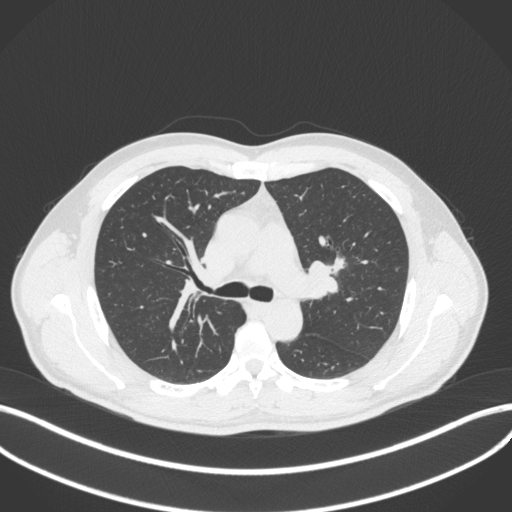
Chest CT, one axial slice. Position 274 of 383 along the scan axis. Reconstruction kernel B31f. Lung window (W 1500 / L -600 HU). 1 mm slice thickness. 512 × 512 image matrix, field of view 400 × 400 mm. Male patient, age 50 years. Case-level facts recorded for this patient, not image findings: clinical TNM (as recorded): T1c N1 M1b.
Annotated regions visible in this slice (bounding box drawn by a radiologist):
- lung tumour (recorded histology: squamous cell carcinoma): bounding box (x1, y1, x2, y2) in pixels: (307, 251, 348, 301)